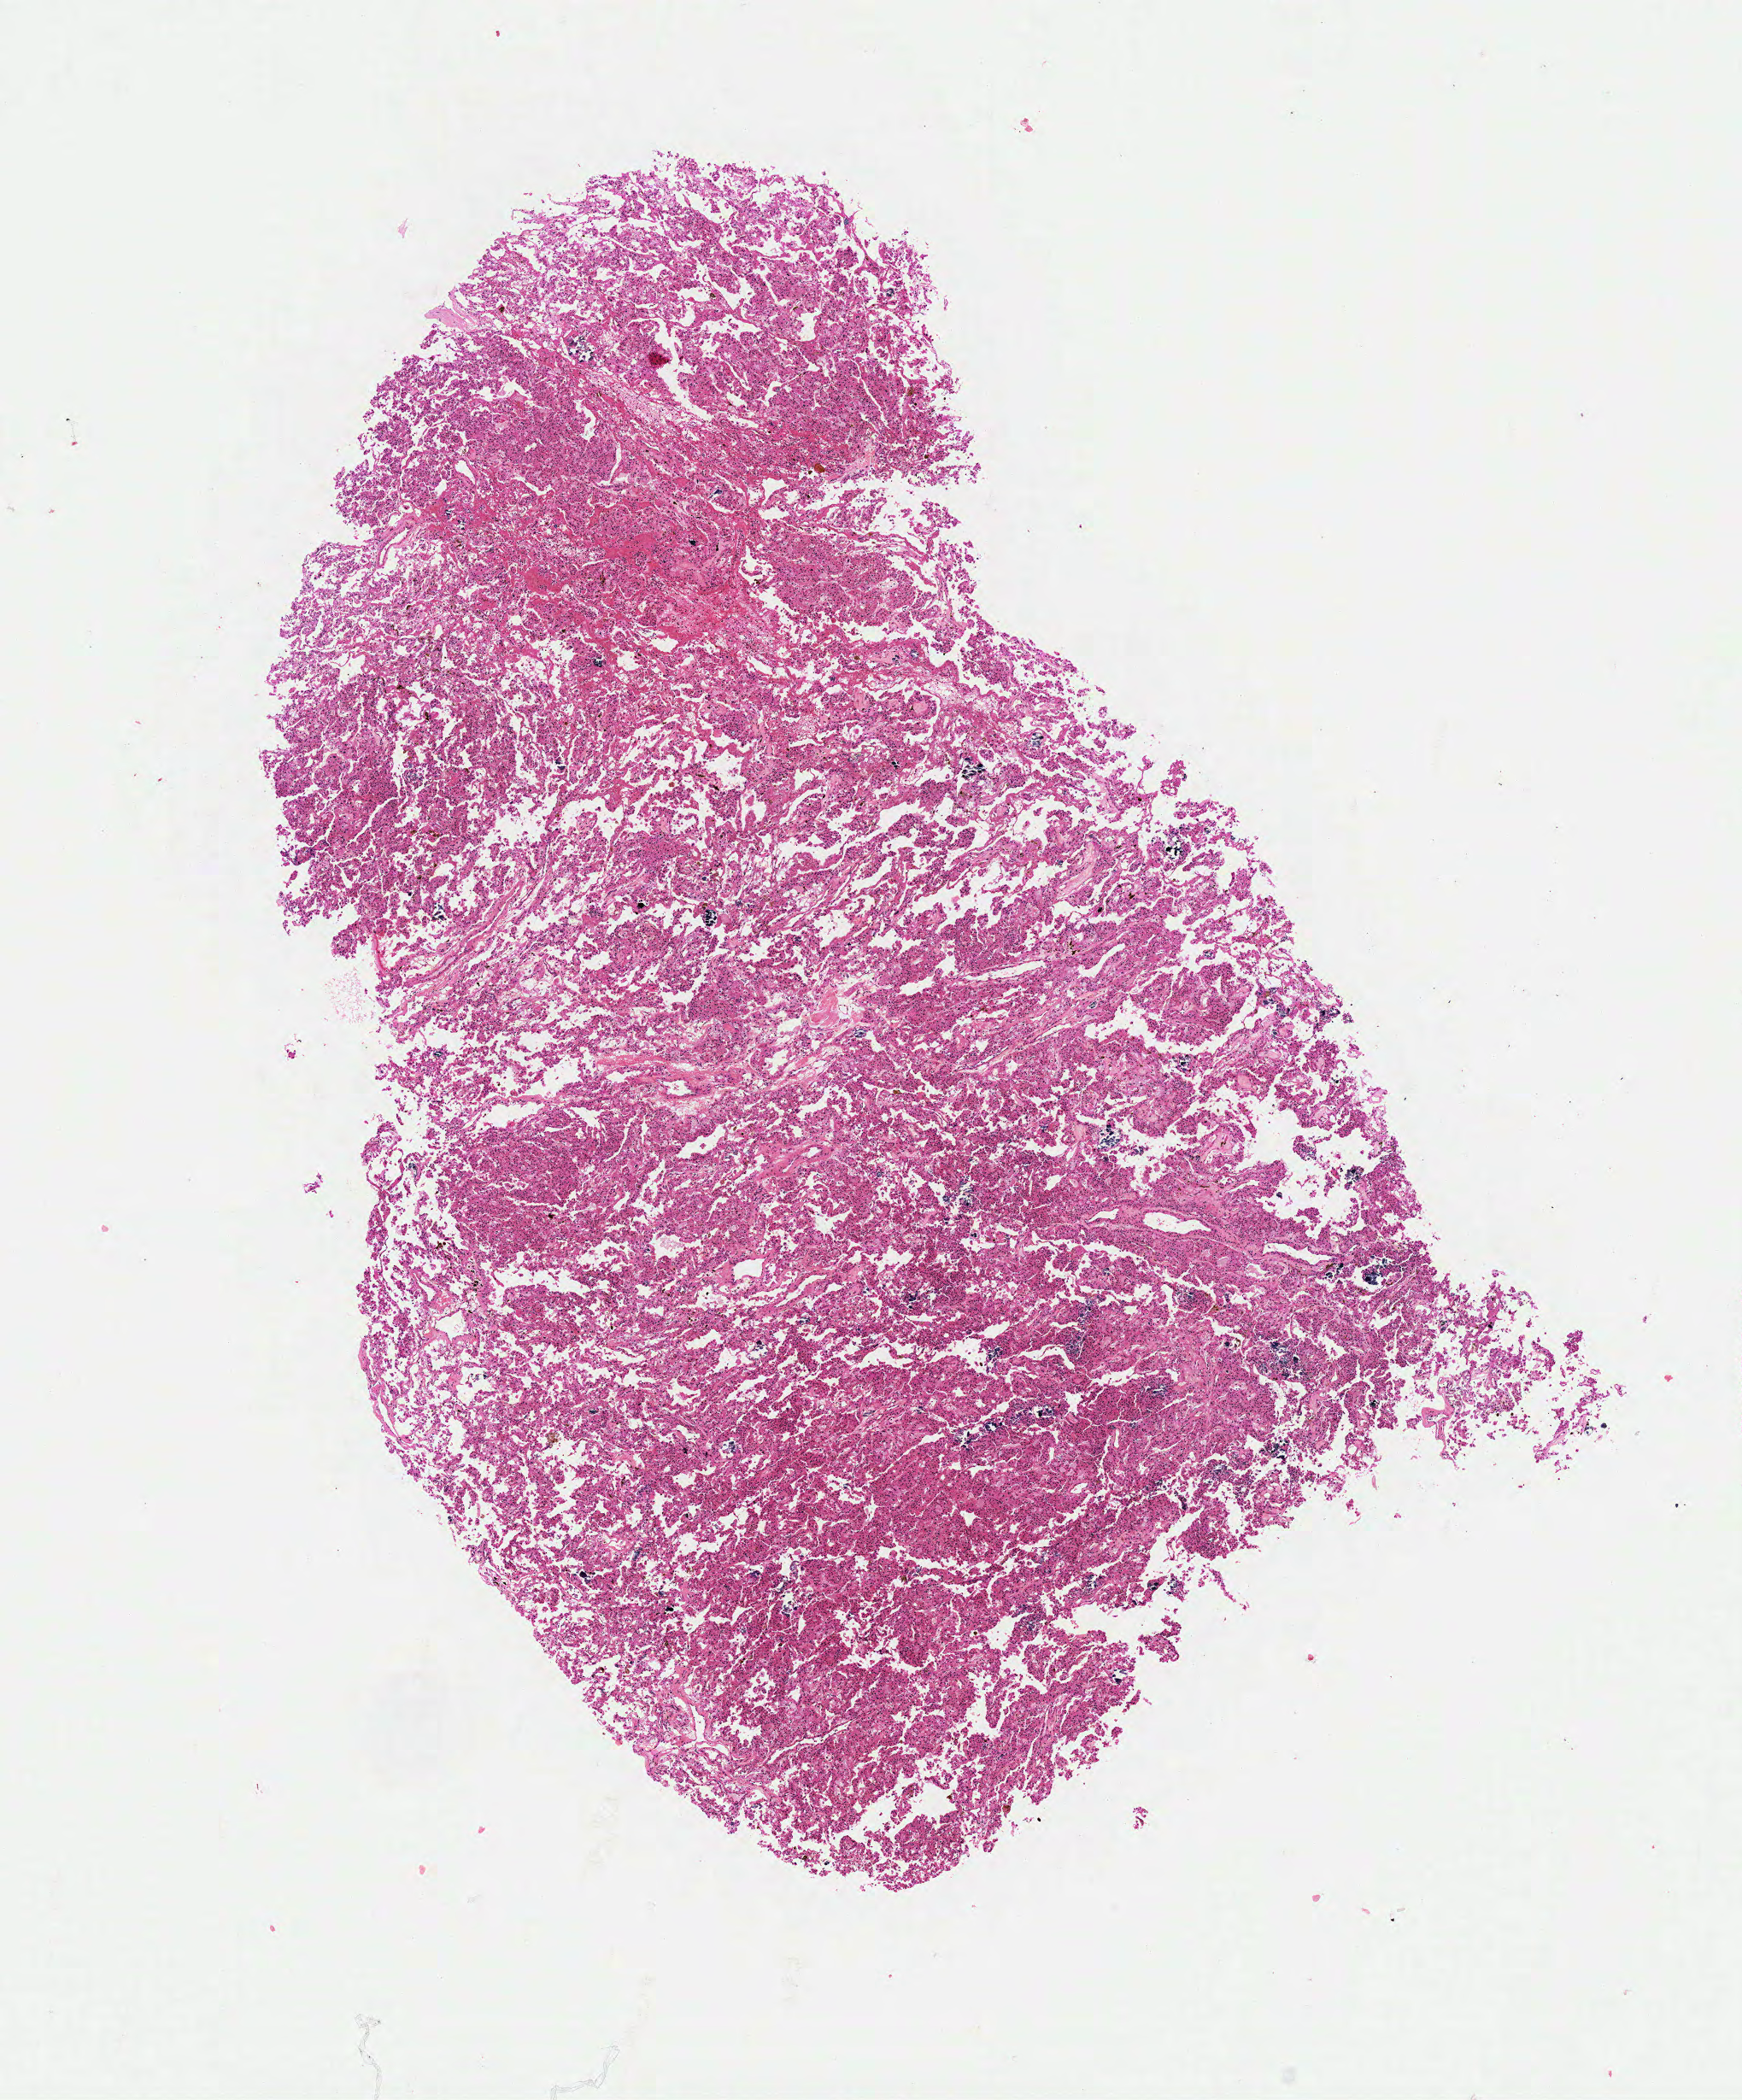
Digitized Hematoxylin and eosin (H&E) stained tissue section (whole slide), whole scanned area (about 8.1 x 9.7 mm, acquisition: 40x scan) shown as a low-resolution overview. FFPE section. Kidney, primary tumour sample. Male patient; age at initial diagnosis 58 years. Histologic grade: G3 (poorly differentiated).
* TNM: T1a NX M0
* laterality: left
* histologic diagnosis: Clear cell adenocarcinoma, NOS
* AJCC pathologic stage: I (6th edition)